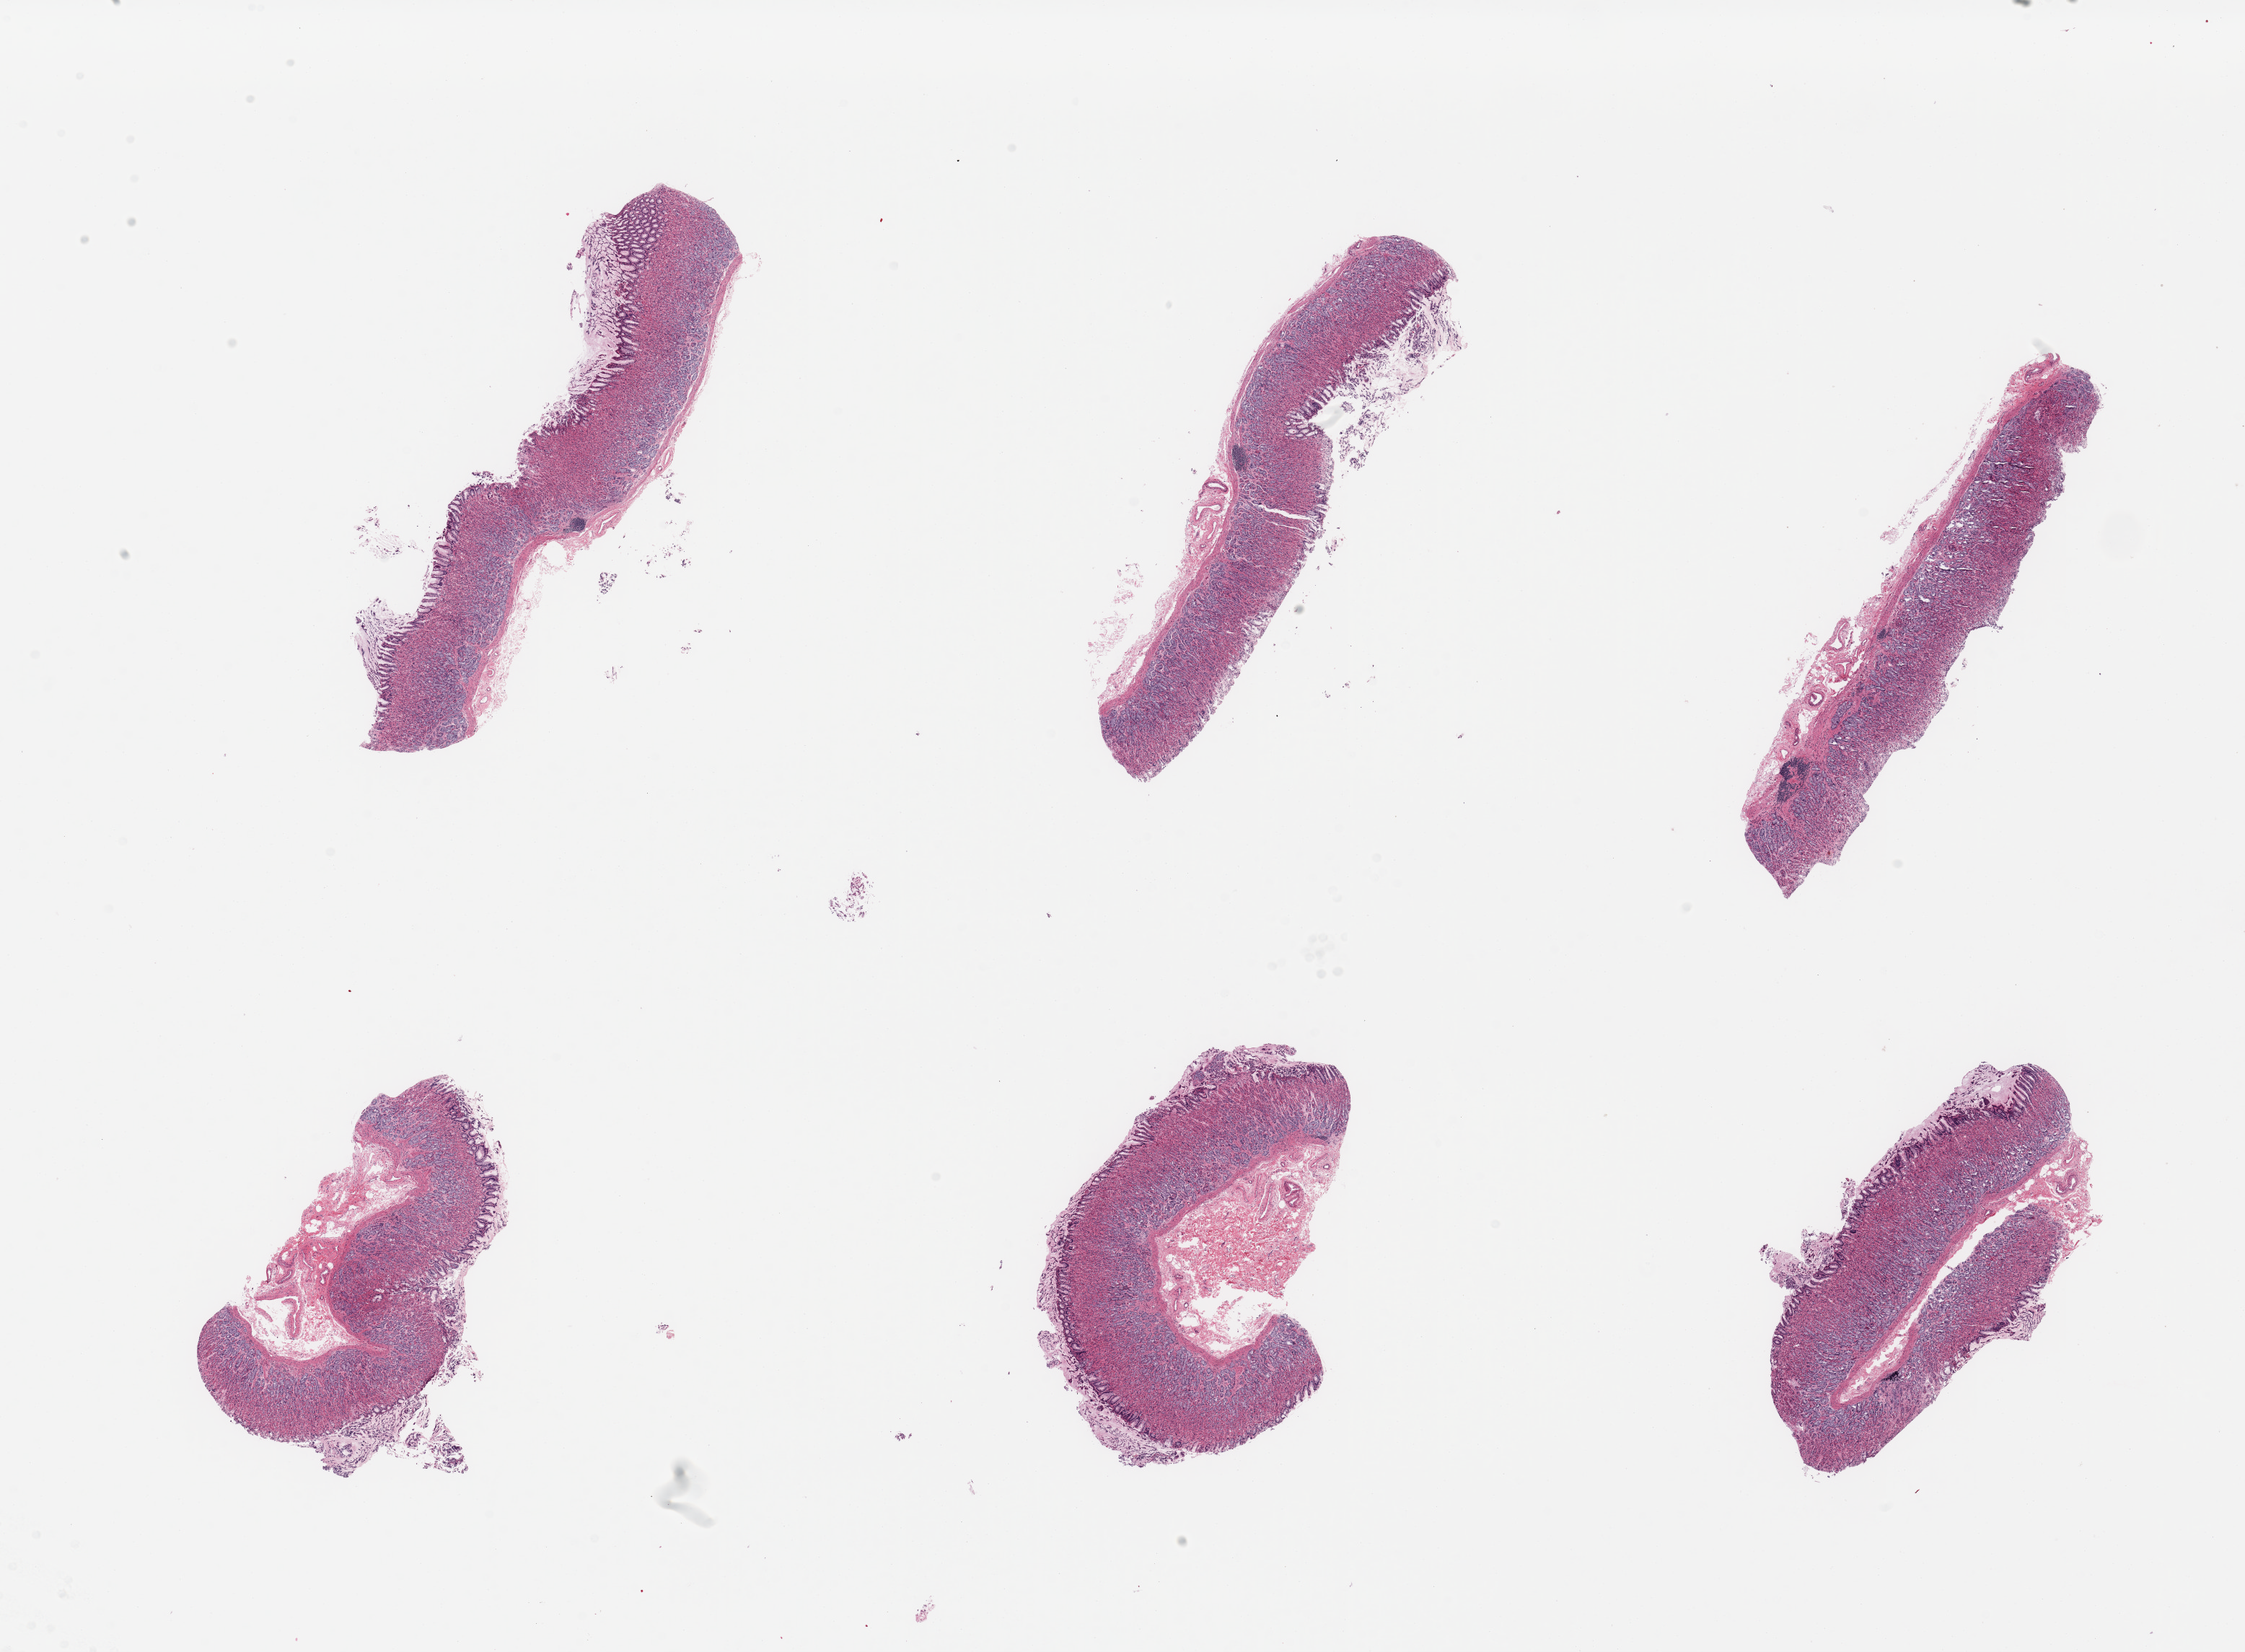
Hematoxylin and eosin (H&E) whole-slide image — shown as a low-resolution overview of the whole scanned area (about 24.6 x 18.1 mm); PAXgene-fixed, paraffin-embedded tissue; section of stomach (target tissue); tissue donor sample.
Review note (as recorded): 6 pieces; gastric mucosa with variable attachment of submucosa.